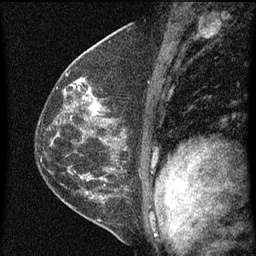
Breast MRI (dynamic contrast-enhanced), one sagittal slice. Dynamic contrast-enhanced series, image 2 of 4 at this slice position (ordered by acquisition). 1.5 T. TE 4.2 ms, TR 8 ms. 2 mm slice thickness. 256 × 256 image matrix, field of view 180 × 180 mm. Female patient, age 48 years.
Annotated regions visible in this slice (semi-automatic segmentation, software-assisted and operator-edited):
- analysis volume of interest (the breast-tissue region the enhancement analysis was run in; not a lesion): bounding box <73,82,115,139> (left, top, right, bottom; pixels)
- tumour enhancement mask (voxels above the 70 % enhancement threshold inside the analysis volume of interest): <73,84,101,139>